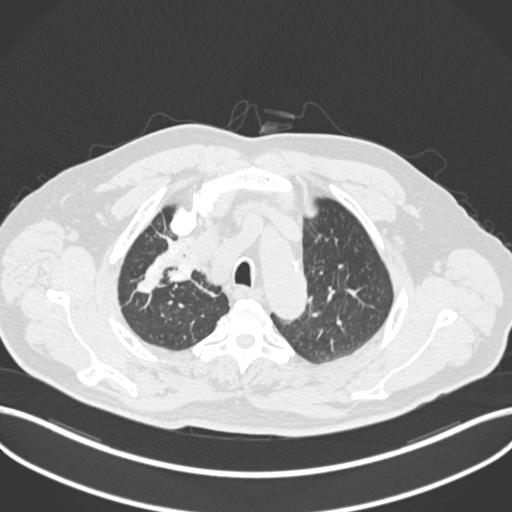
Chest CT, one axial slice; position 164 of 255 along the scan axis; 120 kVp; lung window (W 1500 / L -600 HU); 1 mm slice thickness; 512 × 512 image matrix, field of view 400 × 400 mm. Patient: male, 60 years. Case-level facts recorded for this patient, not image findings: clinical TNM (as recorded): T1b N1 M0.
Outlined on this slice (rectangle marked by the reading radiologist):
- lung tumour (recorded histology: squamous cell carcinoma): box from (x=162, y=243) to (x=201, y=290) px